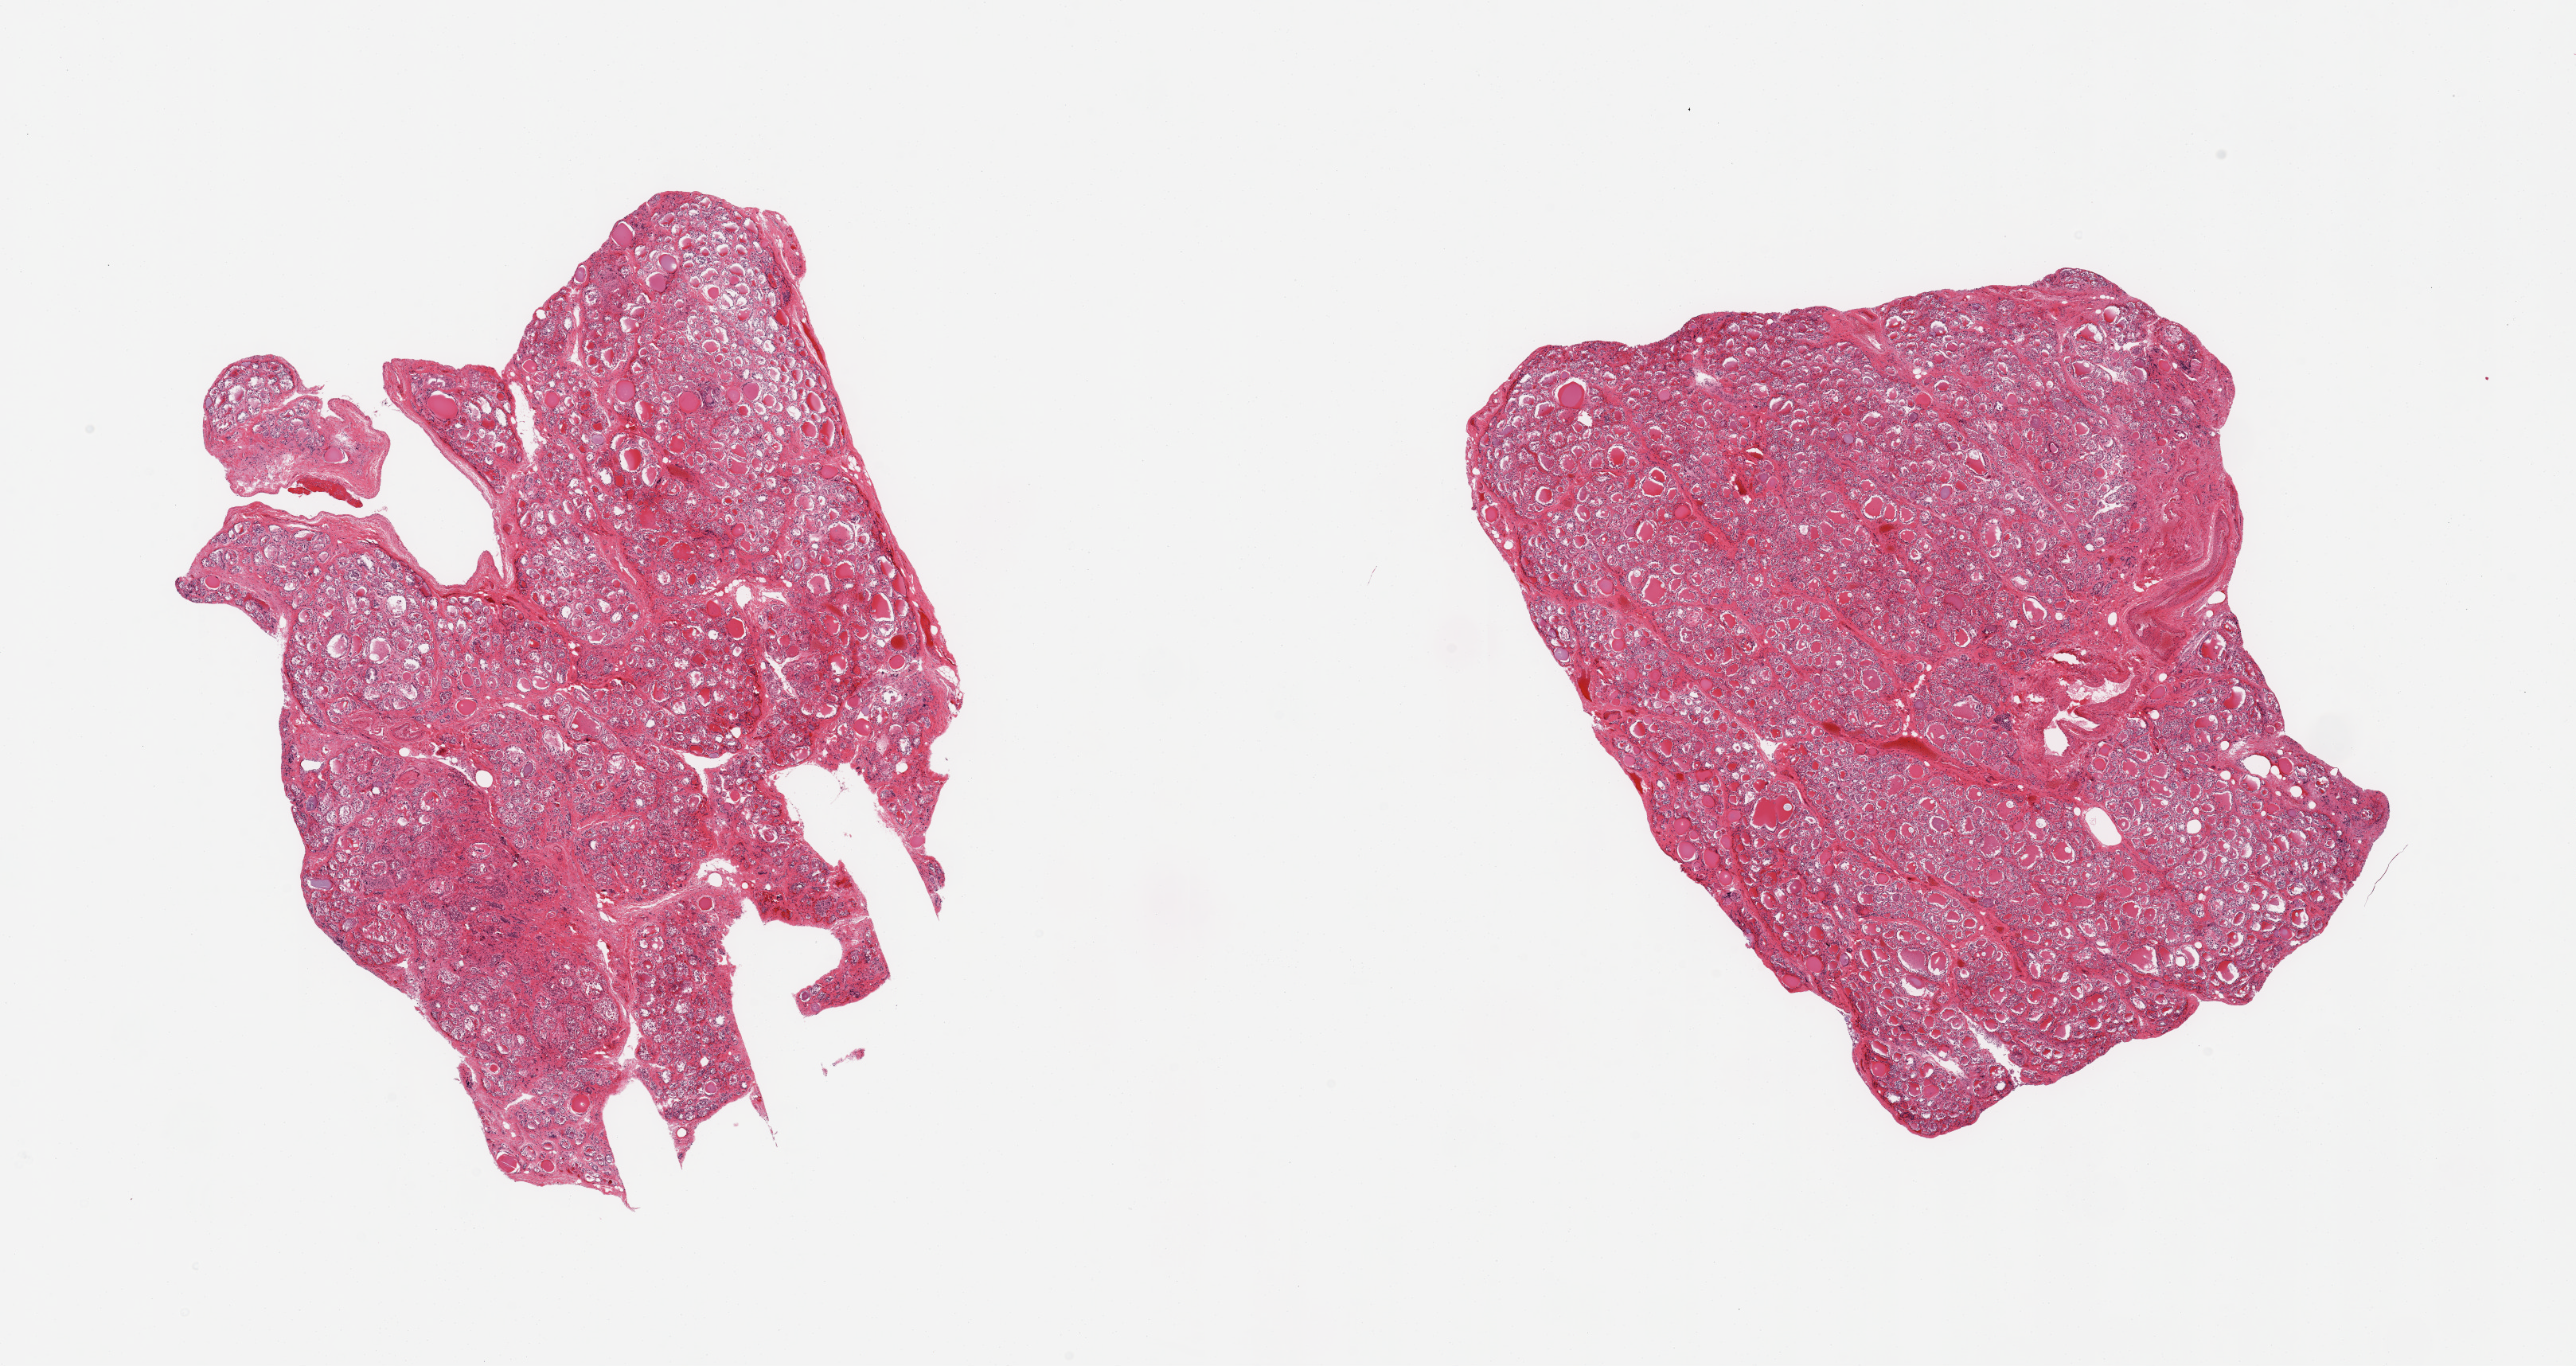
Hematoxylin and eosin (H&E) whole-slide image — a low-resolution overview of the entire scanned area, about 25.6 x 13.6 mm (slide scanned at 20x), PAXgene-fixed, paraffin-embedded tissue, sampled site (target tissue): thyroid, donor tissue sample. Donor sex: male.
Review note (as recorded): 2 pieces, regressive changes, micronodular goitre.